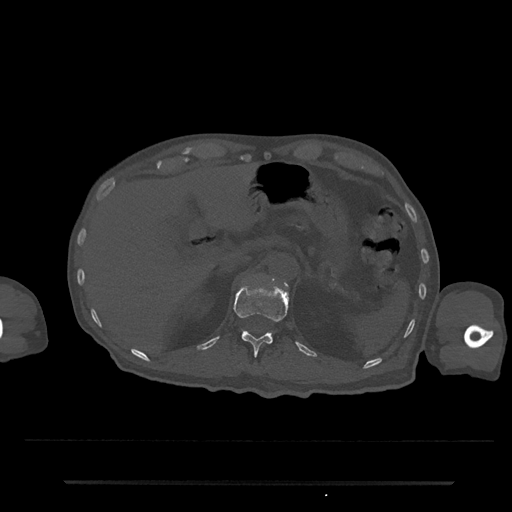
CT including the spine, one axial slice. Slice 186 of 797 in the series (ordered by position). Reconstruction kernel Br40s/3. 120 kVp. Bone window (W 1800 / L 400 HU). 0.5 mm slice thickness. 512 × 512 image matrix, field of view 427 × 427 mm. Patient: male, 74 years. Case-level facts recorded for this patient, not image findings: primary cancer: prostate.
Structures marked on this image (semi-automatic segmentation, software-assisted and operator-edited):
- T12 vertebra: bounding box [x1, y1, x2, y2] px = [234, 284, 289, 356]